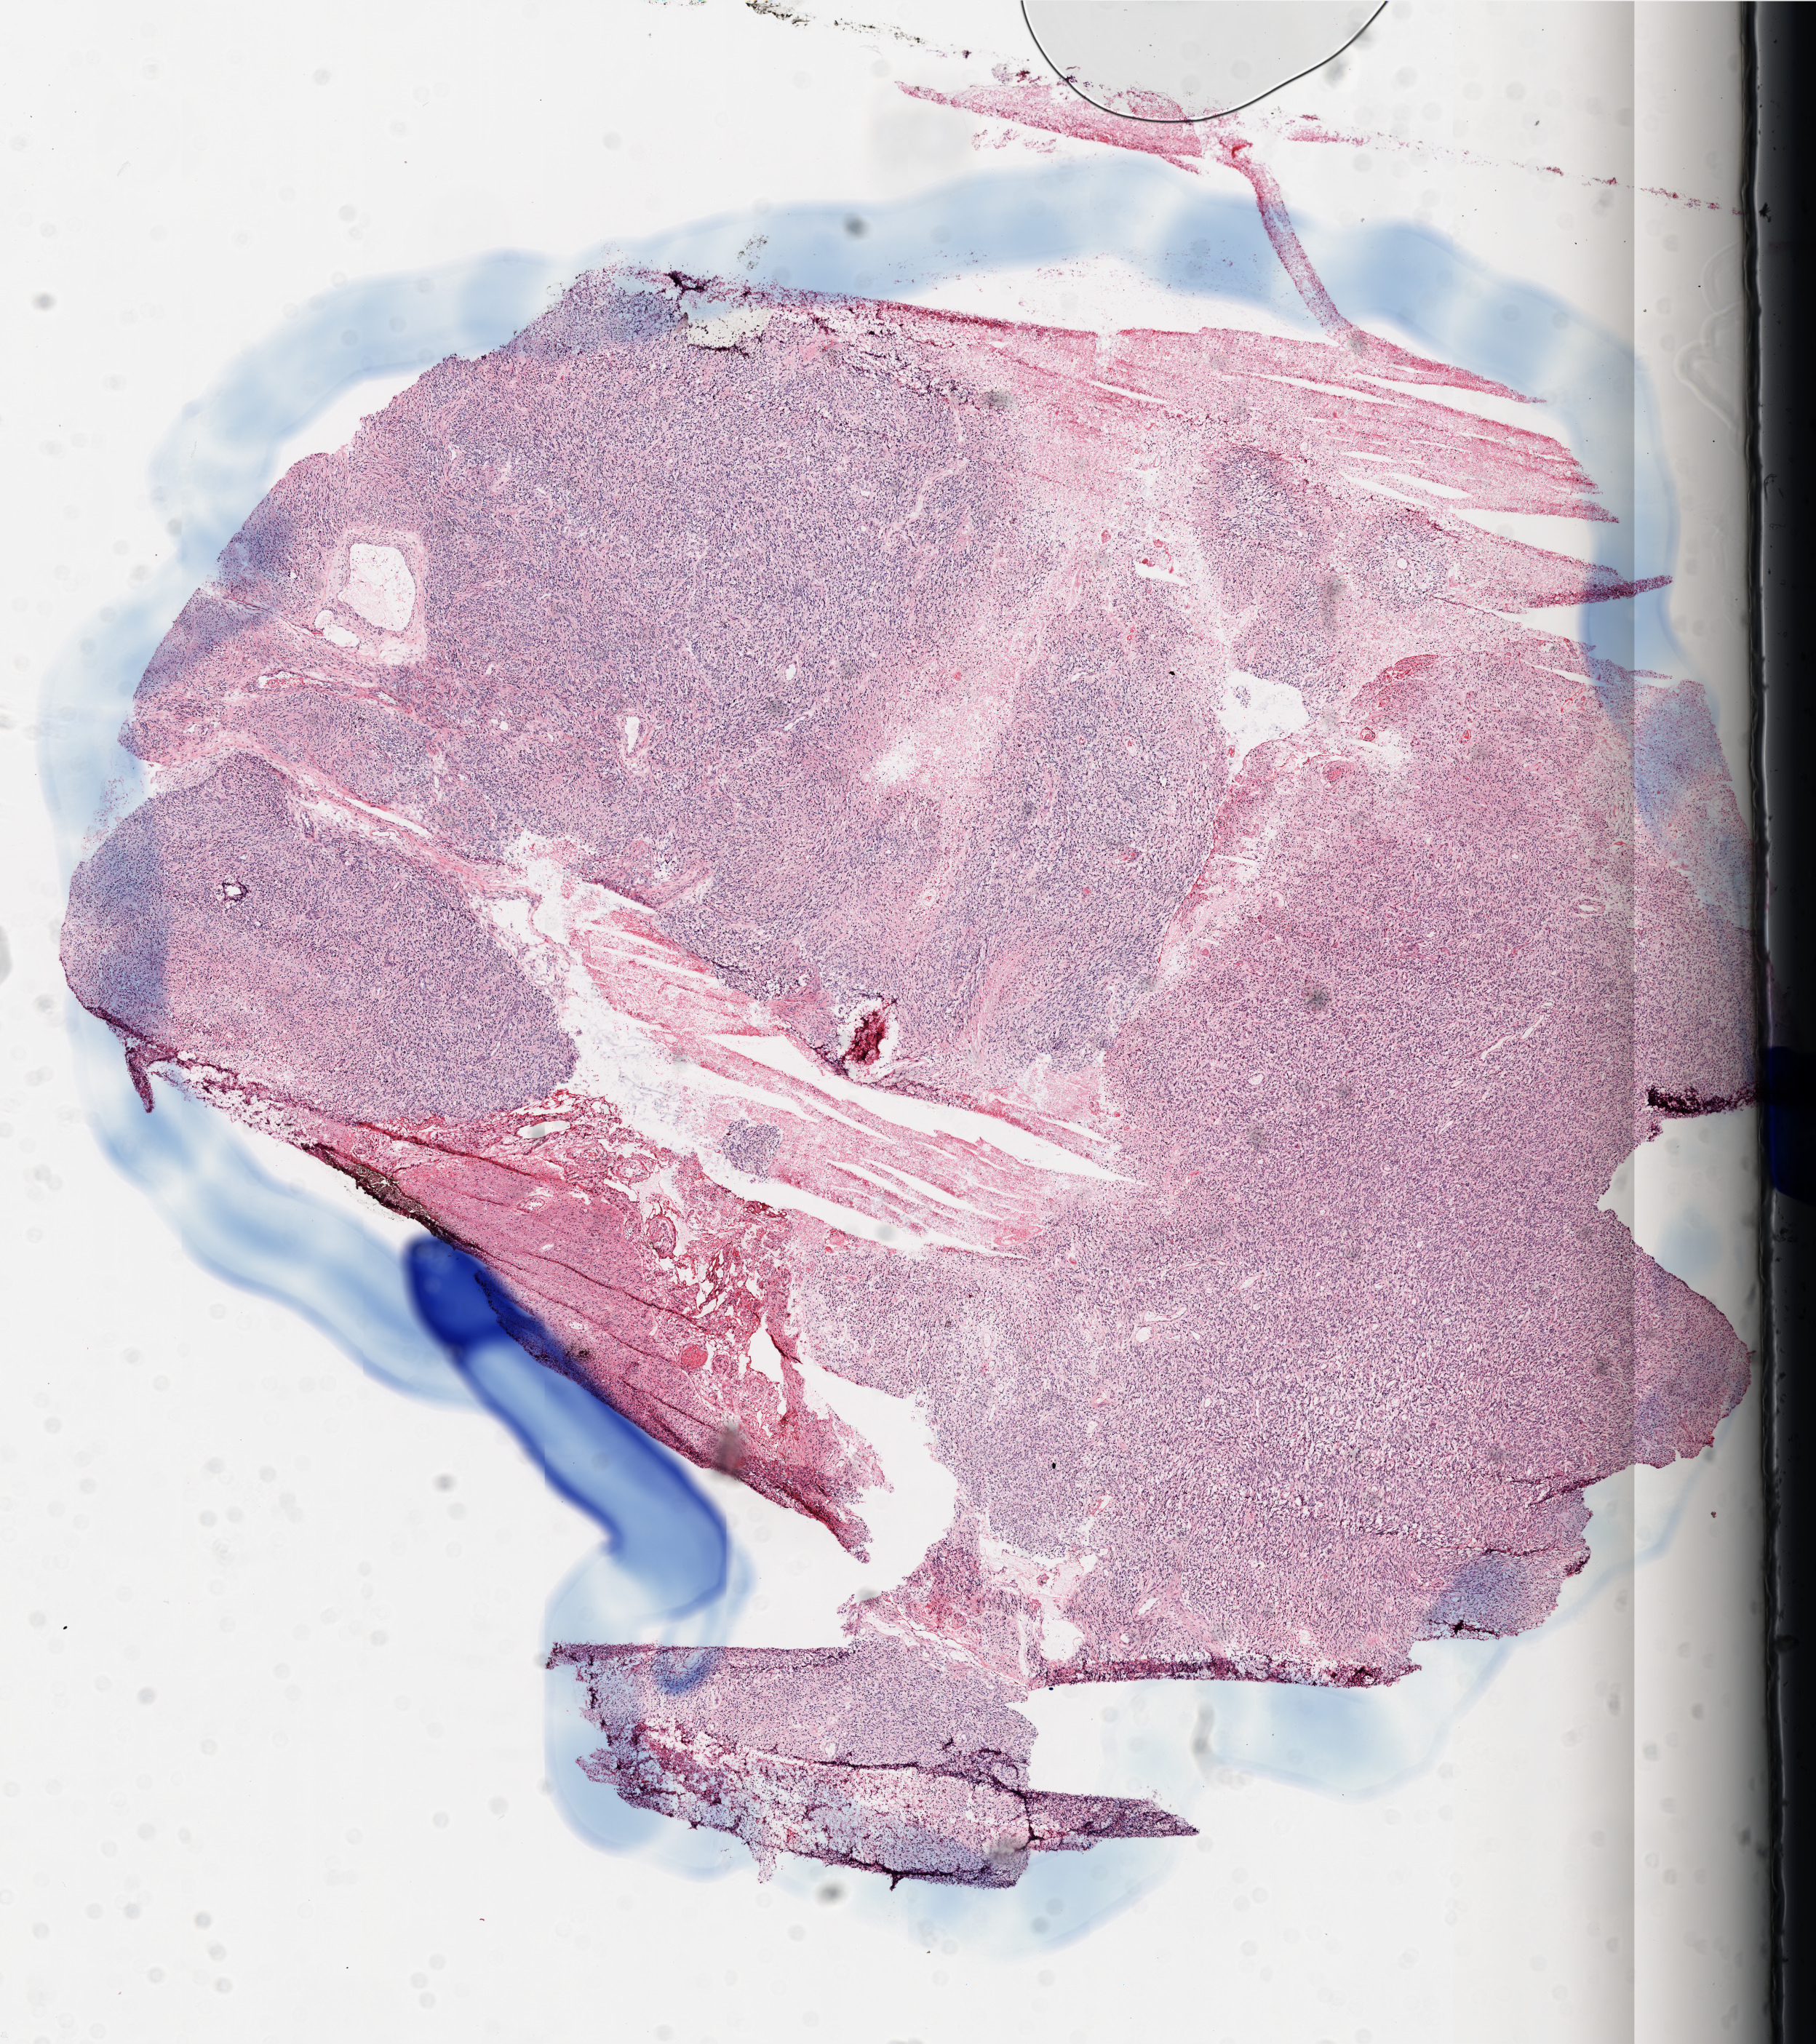
Digitized H&E tissue section (whole slide), a low-resolution overview of the entire scanned area, about 10.0 x 11.2 mm (acquisition: 20x scan); frozen section; sample: primary tumour, brain. Male, age 76 years at initial diagnosis. Pathologist review of this section (percent, as recorded): tumour cells 90%, tumour nuclei 100%, normal cells 0%, stromal cells 0%, necrosis 10%. Inflammatory infiltration, as recorded: lymphocyte infiltration 0%, monocyte infiltration 0%, neutrophil infiltration 0%.
Diagnosis: Glioblastoma.